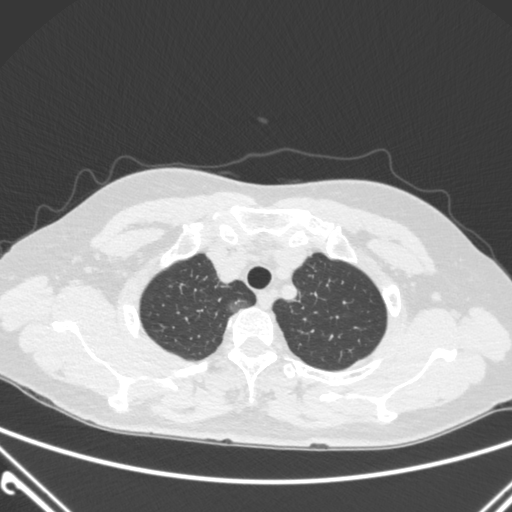
Chest CT, one axial slice. 120 kVp. Lung window (W 1500 / L -600 HU). 1 mm slice thickness. 512 × 512 image matrix. Patient: female, 54 years. Case-level facts recorded for this patient, not image findings: clinical TNM (as recorded): T1a N0 M0.
Outlined on this slice (bounding box drawn by a radiologist):
- lung tumour (recorded histology: adenocarcinoma): bounding box <225,294,252,318> (left, top, right, bottom; pixels)